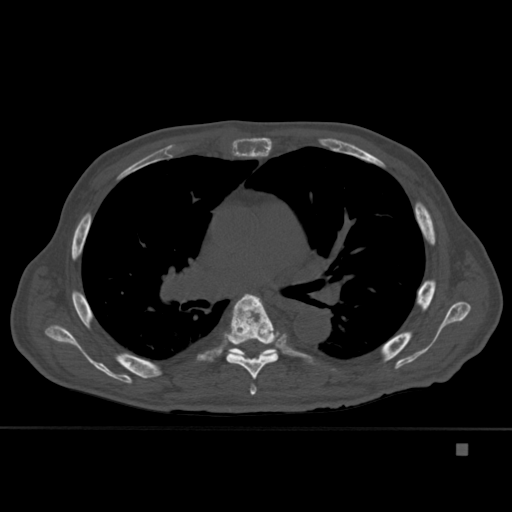
CT including the spine, one axial slice; slice 292 of 451 in the series (ordered by position); bone window (W 1800 / L 400 HU); 1.5 mm slice thickness; 512 × 512 image matrix. Male patient, age 75 years. From the clinical record (not read from this slice): primary cancer: prostate.
Outlined on this slice (semi-automatic segmentation, software-assisted and operator-edited):
- T5 vertebra: box from (x=250, y=383) to (x=257, y=395) px
- T6 vertebra: (x=224, y=294)–(x=279, y=379)
- T7 vertebra: (x=229, y=347)–(x=278, y=357)